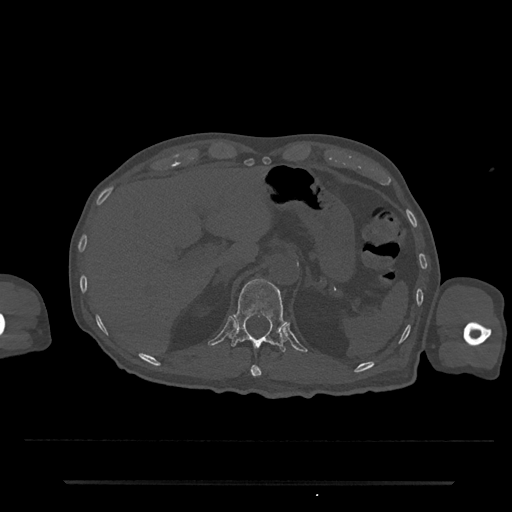
CT including the spine, one axial slice; slice 201 of 797 in the series (ordered by position); bone window (W 1800 / L 400 HU); 0.5 mm slice thickness; 512 × 512 image matrix, field of view 427 × 427 mm. Patient: male, 74 years. From the clinical record (not read from this slice): primary cancer: prostate.
Annotated regions visible in this slice (semi-automatic segmentation, software-assisted and operator-edited):
- T11 vertebra: bounding box (x1, y1, x2, y2) in pixels: (250, 365, 262, 377)
- T12 vertebra: (229, 278, 287, 352)